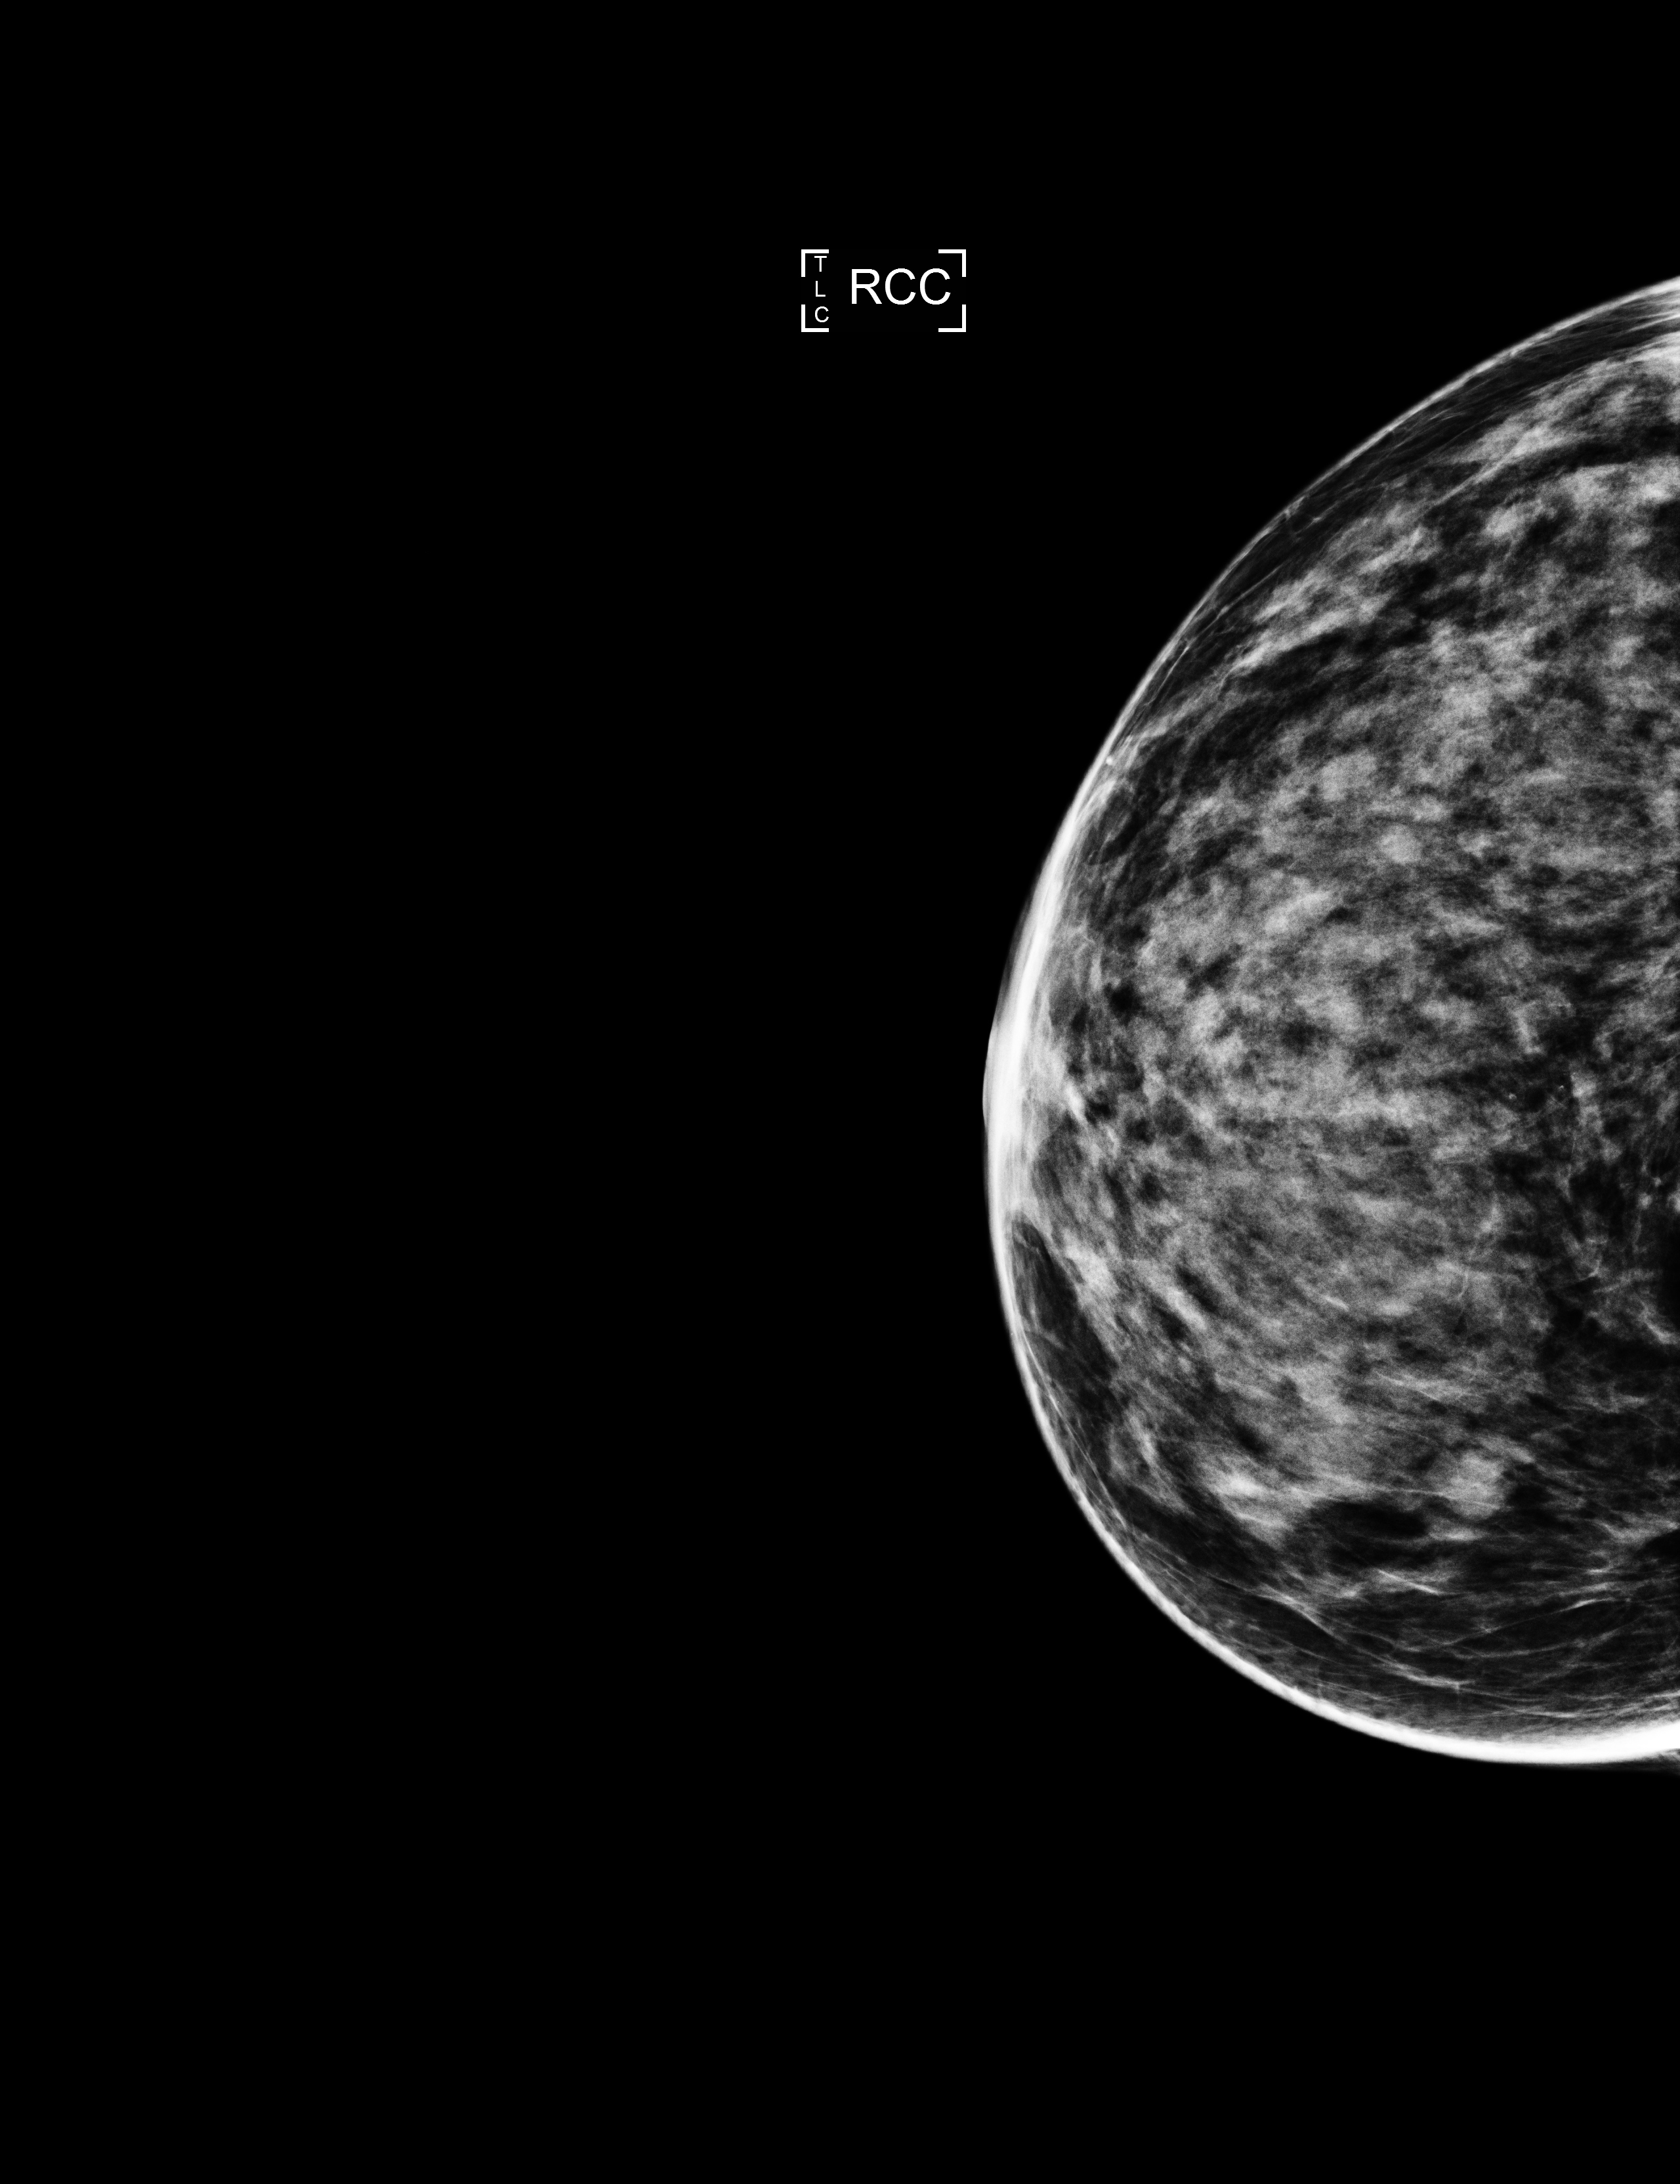
Annual screening mammography examination, compressed breast thickness 48 mm, system: Selenia Dimensions. Female patient, age 53 years.
Image type: full-field digital mammogram. Breast: right. Projection: CC view.